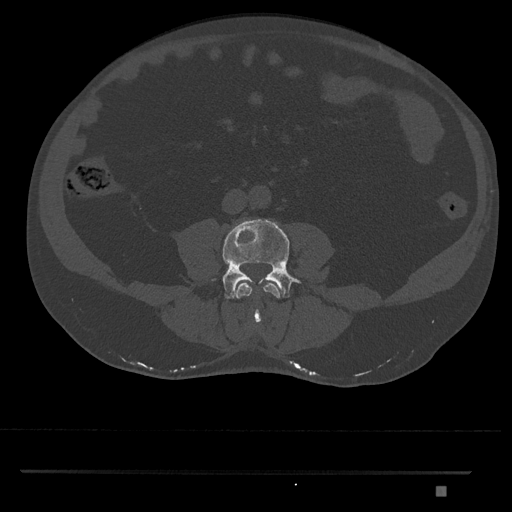
CT including the spine, one axial slice. Position 637 of 1134 along the scan axis. 120 kVp. Bone window (W 1800 / L 400 HU). 0.5 mm slice thickness. 512 × 512 image matrix. Patient: male, 65 years. Case-level facts recorded for this patient, not image findings: primary cancer: prostate.
Structures marked on this image (semi-automatically segmented with operator editing):
- L3 vertebra: bounding box (x1, y1, x2, y2) in pixels: (236, 281, 280, 324)
- L4 vertebra: (222, 219, 300, 299)